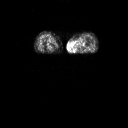
FDG PET of an extremity soft-tissue mass (from a PET/CT study), one axial slice. Position 5 of 91 along the scan axis. 3.27 mm slice thickness. 128 × 128 image matrix, field of view 700 × 700 mm. Patient: female, 74 years. From the clinical record (not read from this slice): histological type: pleomorphic leiomyosarcoma; grade: high; site of the primary tumour: left thigh.
Structures marked on this image (expert contour drawn on MRI and transferred to this co-registered scan by the dataset authors):
- gross tumour volume including surrounding oedema: box from (x=72, y=37) to (x=87, y=50) px